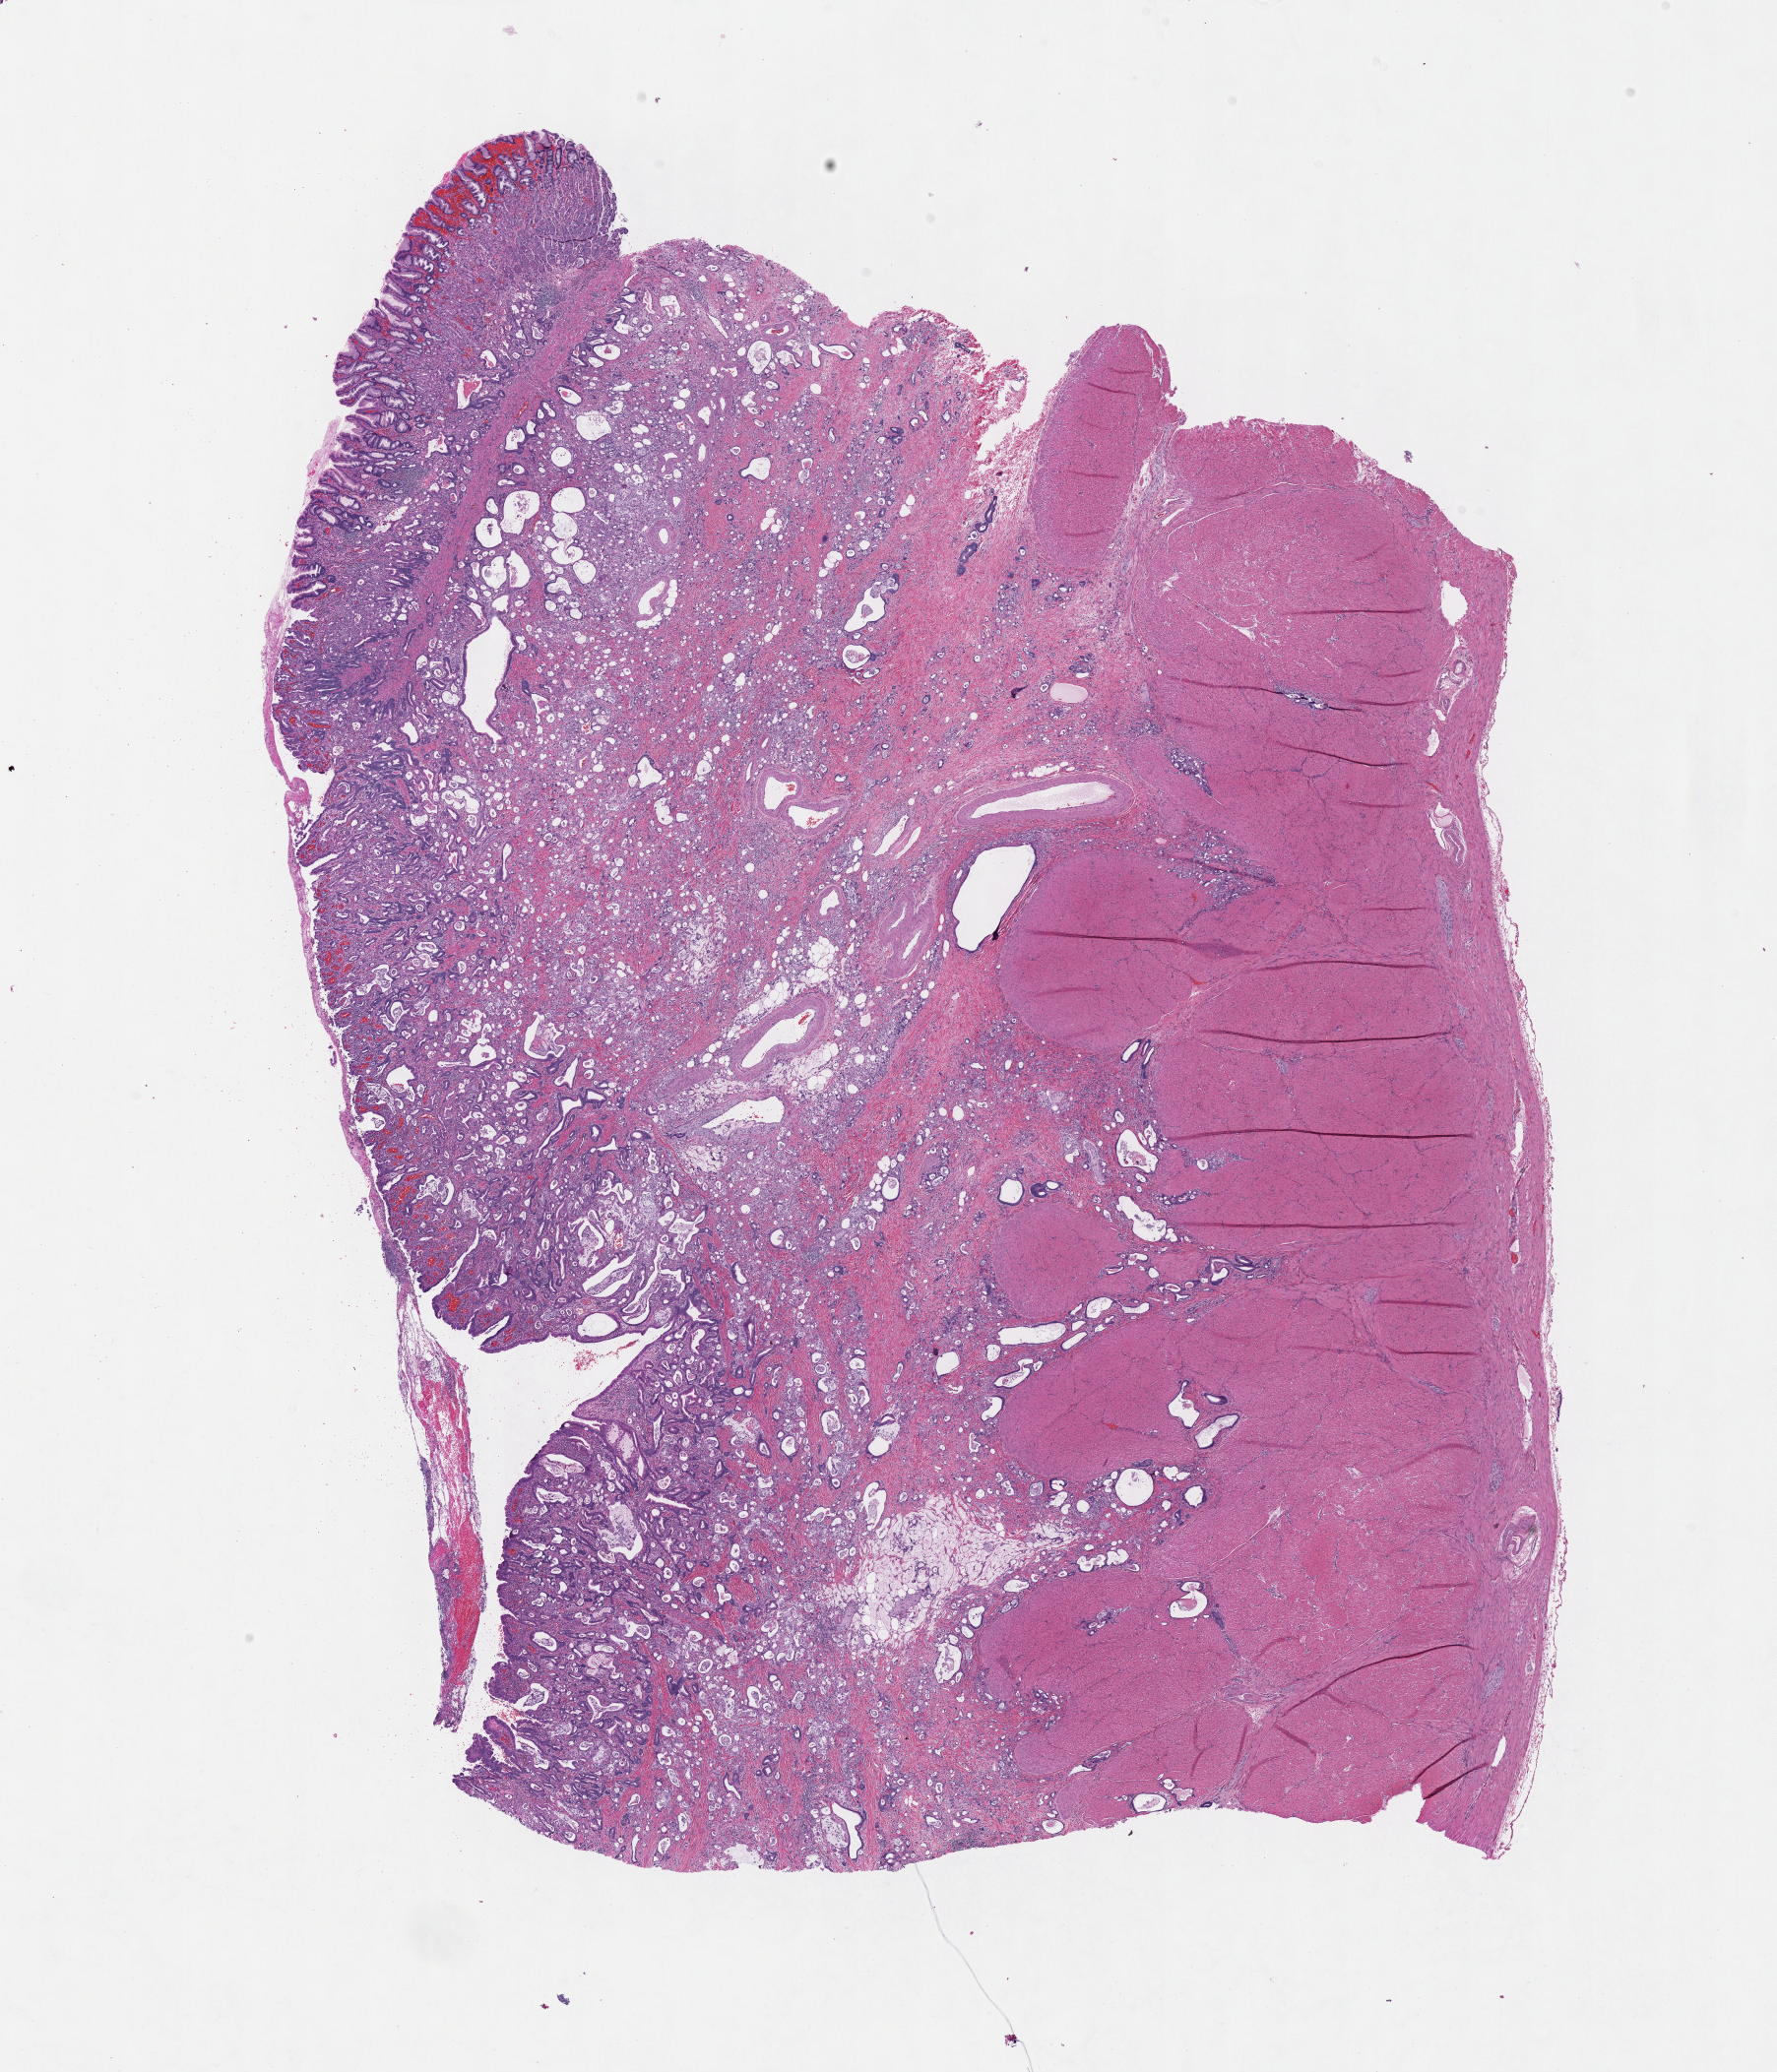
Digitized H&E tissue section (whole slide) — low-resolution overview of the scanned area, about 14.6 x 17.0 mm; formalin-fixed paraffin-embedded (FFPE) diagnostic section; sample: primary tumour, stomach. Male patient; age at initial diagnosis 71 years.
Diagnosis: Adenocarcinoma, intestinal type (gastric antrum).